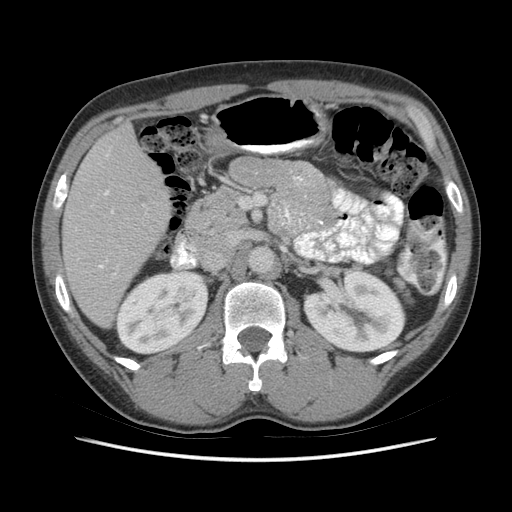
Contrast-enhanced abdominal CT (liver protocol), one axial slice. Position 26 of 73 along the scan axis. Soft-tissue window (W 400 / L 40 HU). 2.5 mm slice thickness. 512 × 512 image matrix. Case-level facts recorded for this patient, not image findings: diagnosis: hepatocellular carcinoma (patient treated with transarterial chemoembolisation; whether this scan precedes or follows treatment is not stated here); TNM stage (as recorded): Stage-IIIA; Child-Pugh class: A; tumour nodularity: multinodular; tumour size: 6.6 cm.
Structures marked on this image (semi-automatic segmentation, software-assisted and operator-edited):
- liver parenchyma outside the tumour (the mass and vessels are separate outlines, so this box may not span the whole liver): bounding box [x1, y1, x2, y2] px = [62, 124, 170, 326]
- liver vessels: [99, 190, 114, 268]